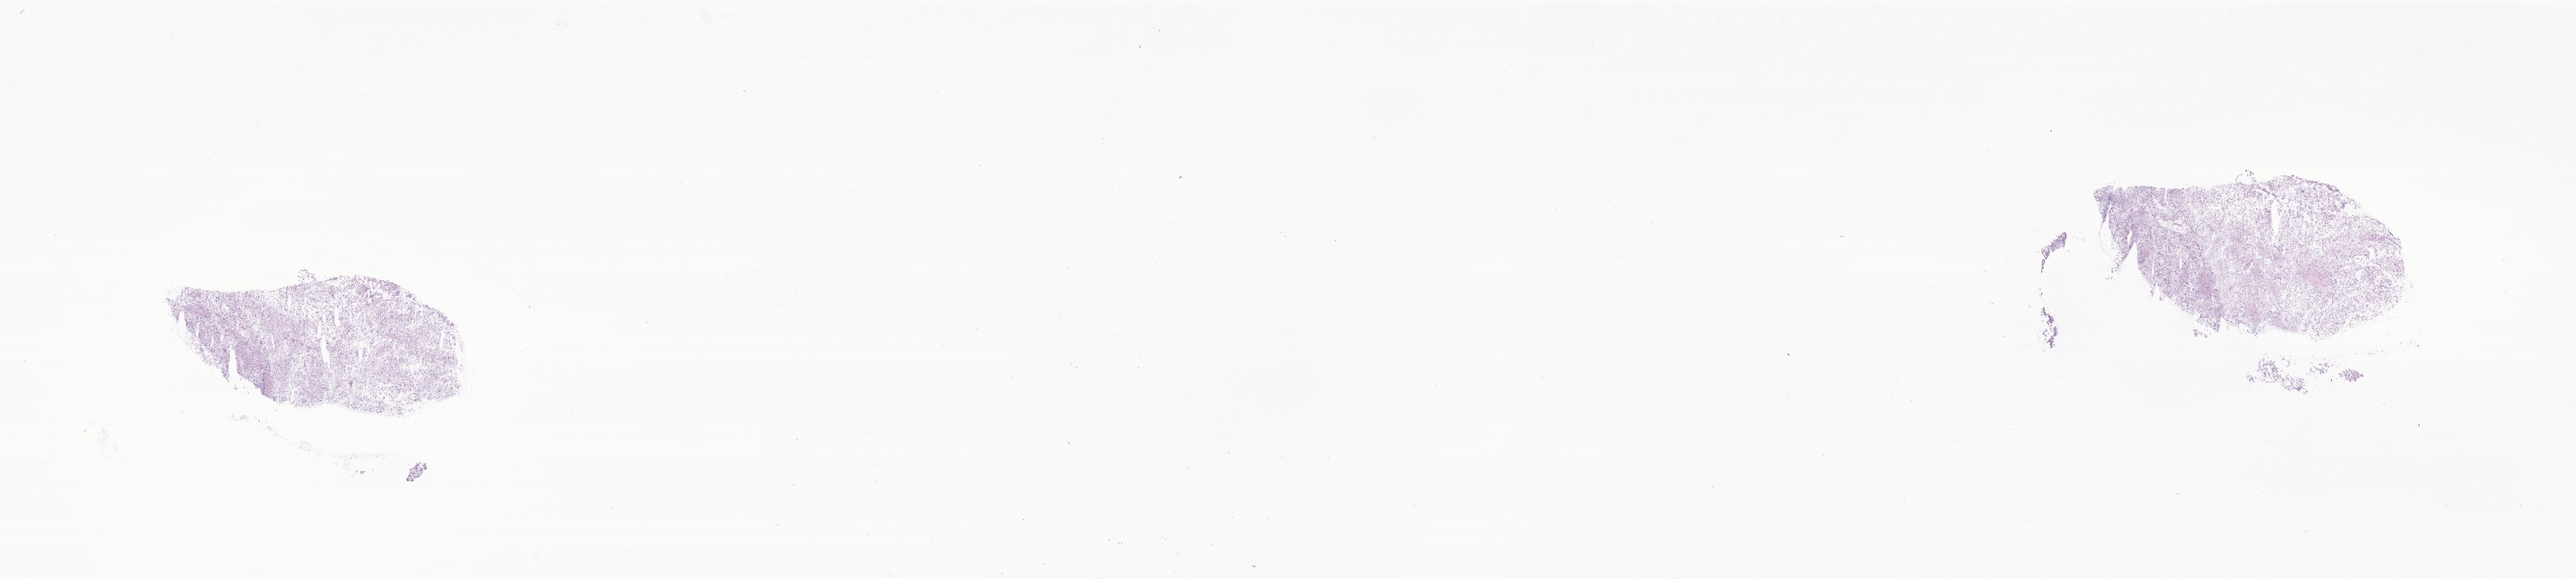
Digitized haematoxylin and eosin-stained section of tumor tissue from the cerebellum — low-resolution overview of the scanned area, about 29.9 x 6.7 mm, frozen section. Female patient, age 135 months (11 years 3 months).
Recorded diagnosis: Pilocytic astrocytoma.